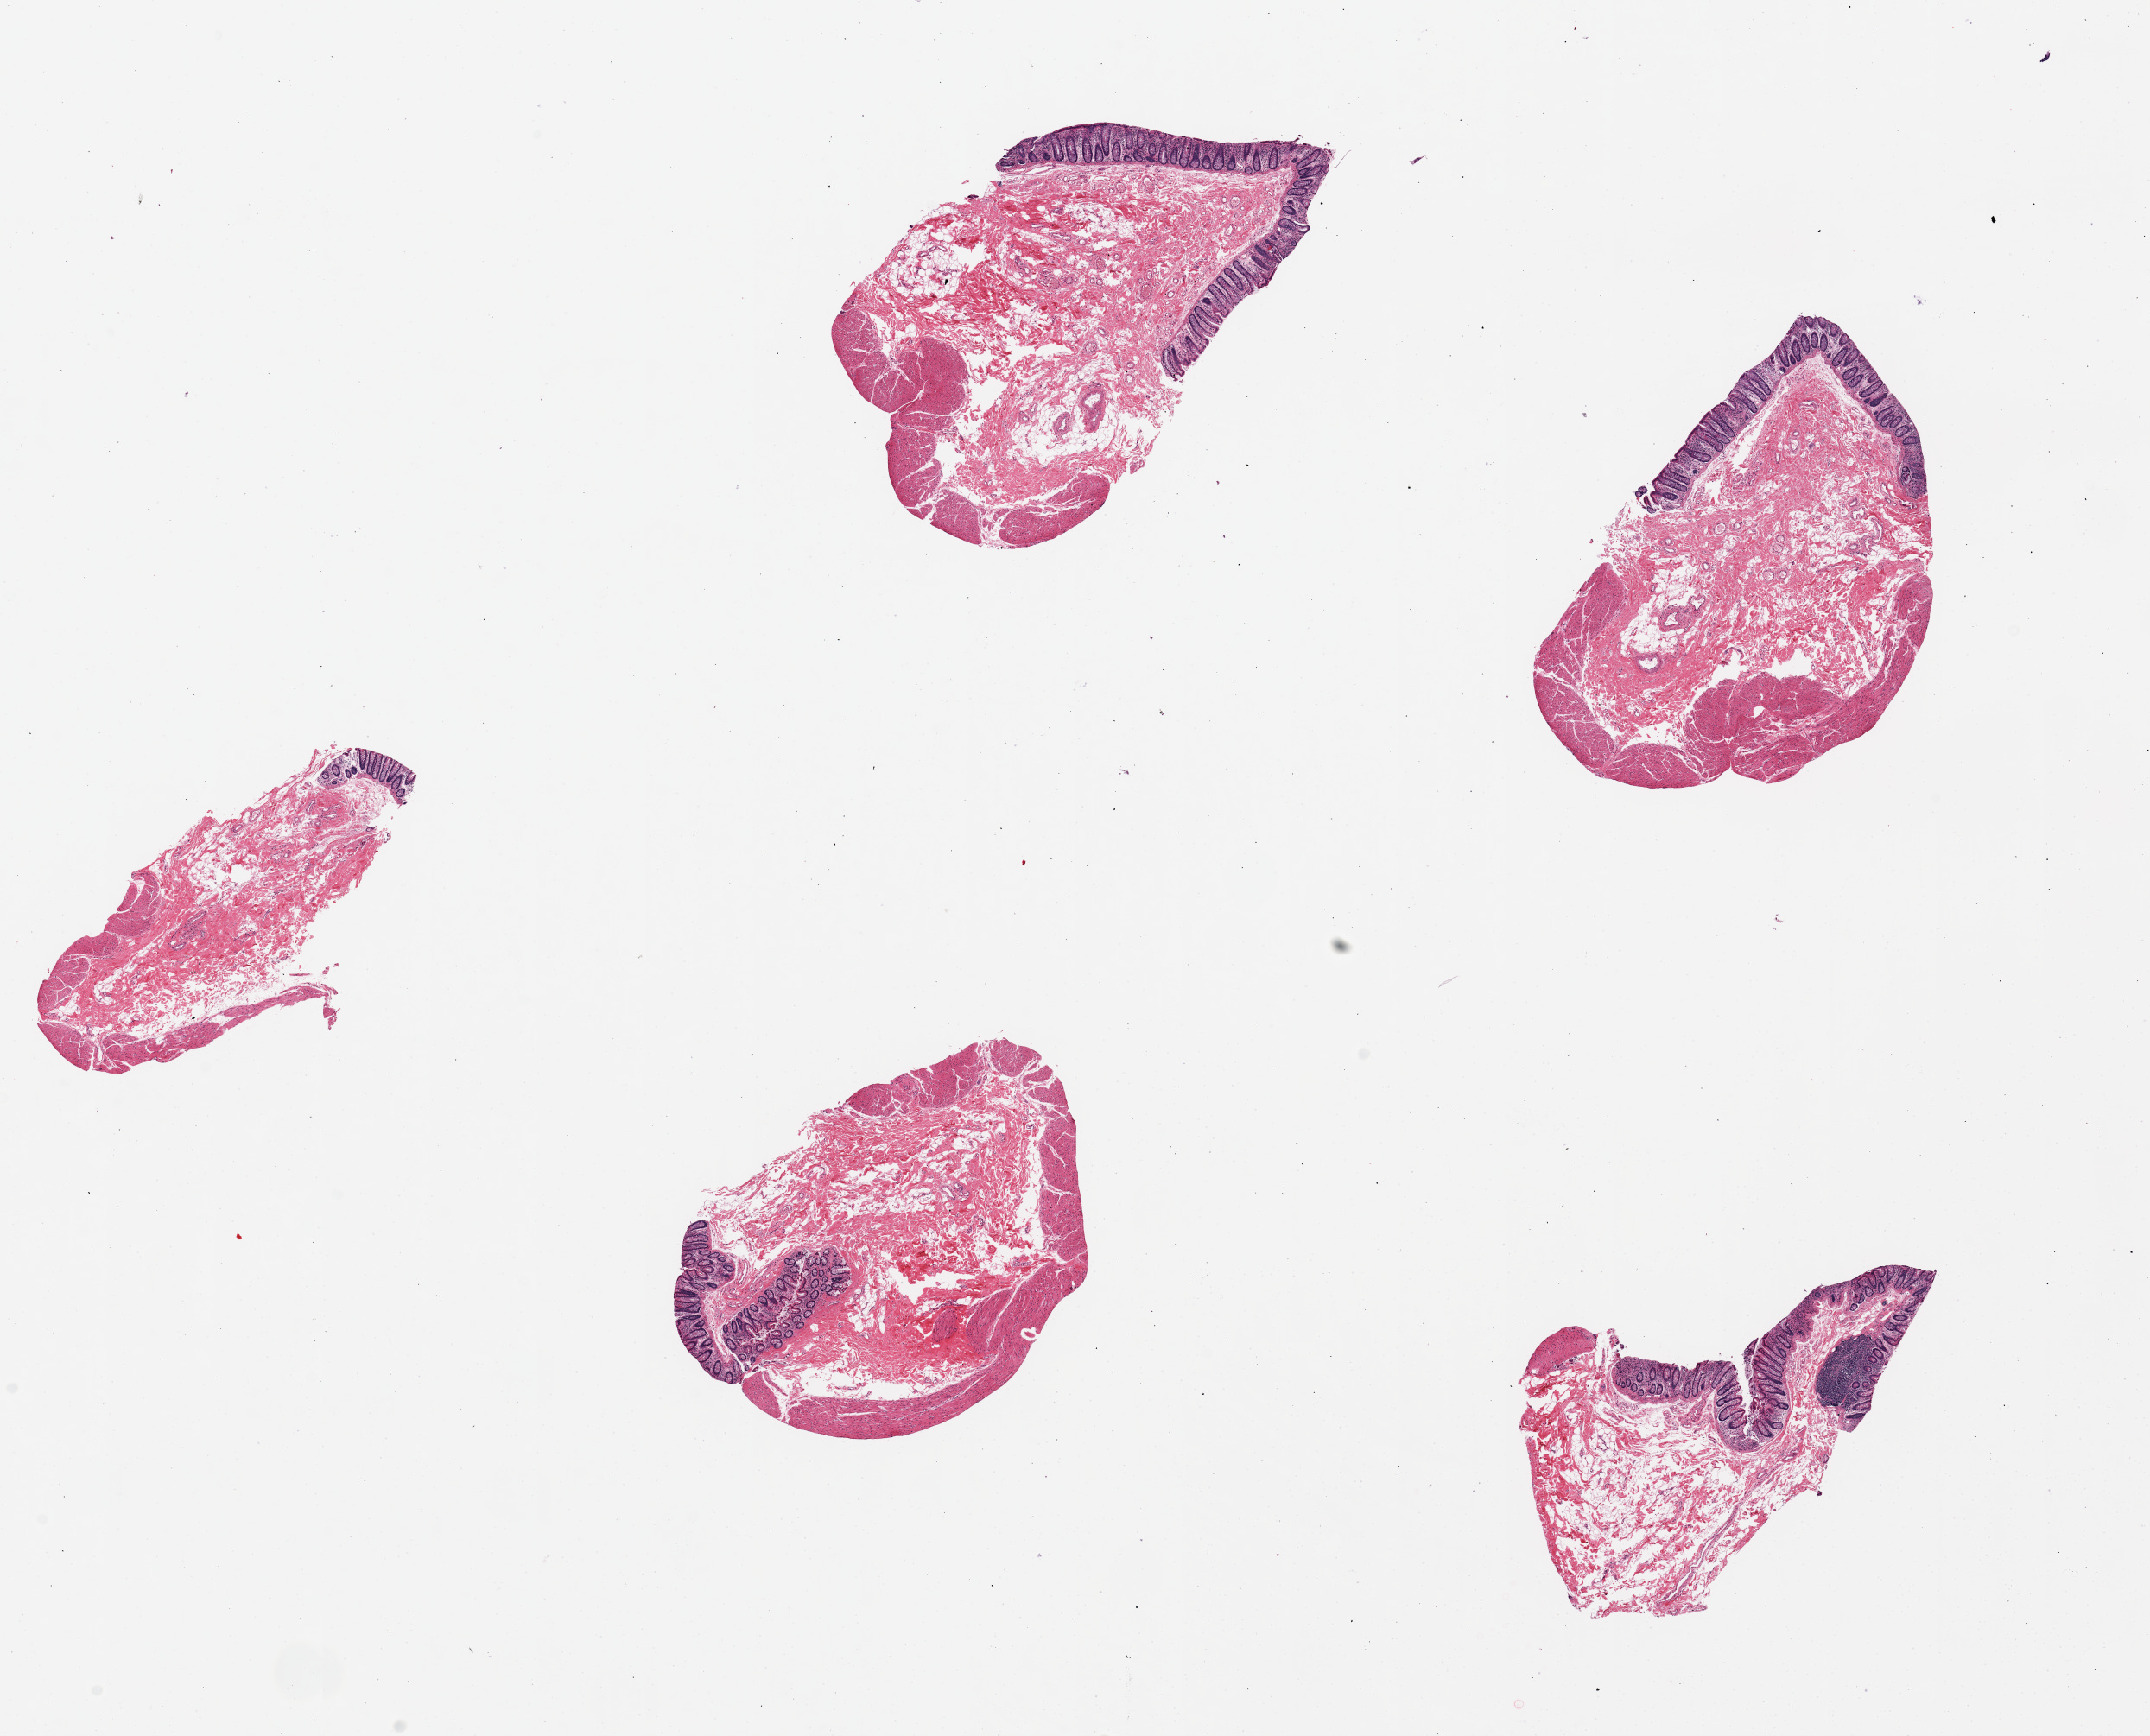
Whole-slide image, haematoxylin and eosin stain, brightfield — shown as a low-resolution overview of the whole scanned area (about 19.7 x 15.9 mm); PAXgene-fixed, paraffin-embedded tissue; target tissue: transverse colon; tissue donor sample. Male donor.
Review note (as recorded): 5 pieces, up to 5x3mm; Mostly submucosa, variable amounts of mucosa and muscularis propria.